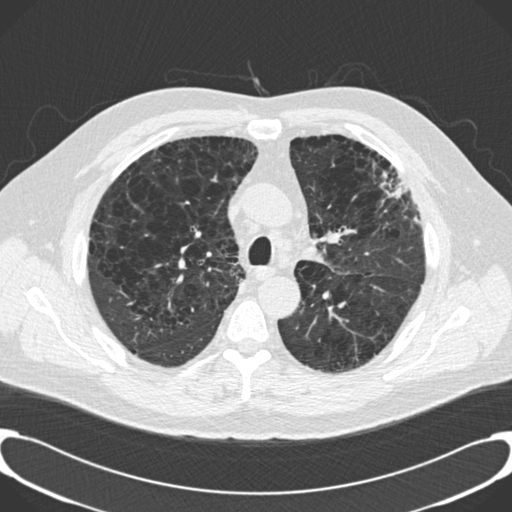
Axial slice from a low-dose chest CT screening exam, third annual screen, lung window (W 1500 / L -600 HU), standard (soft-tissue) reconstruction kernel (B30f), slice 50 of 189 in the series, 512 × 512 image matrix. Male participant, aged 59 years at enrolment.
Expert-annotated lung lesion, bounding box <358,148,420,220> (left, top, right, bottom; pixels). Screening reader's record for this exam: no non-calcified nodule ≥4 mm recorded.